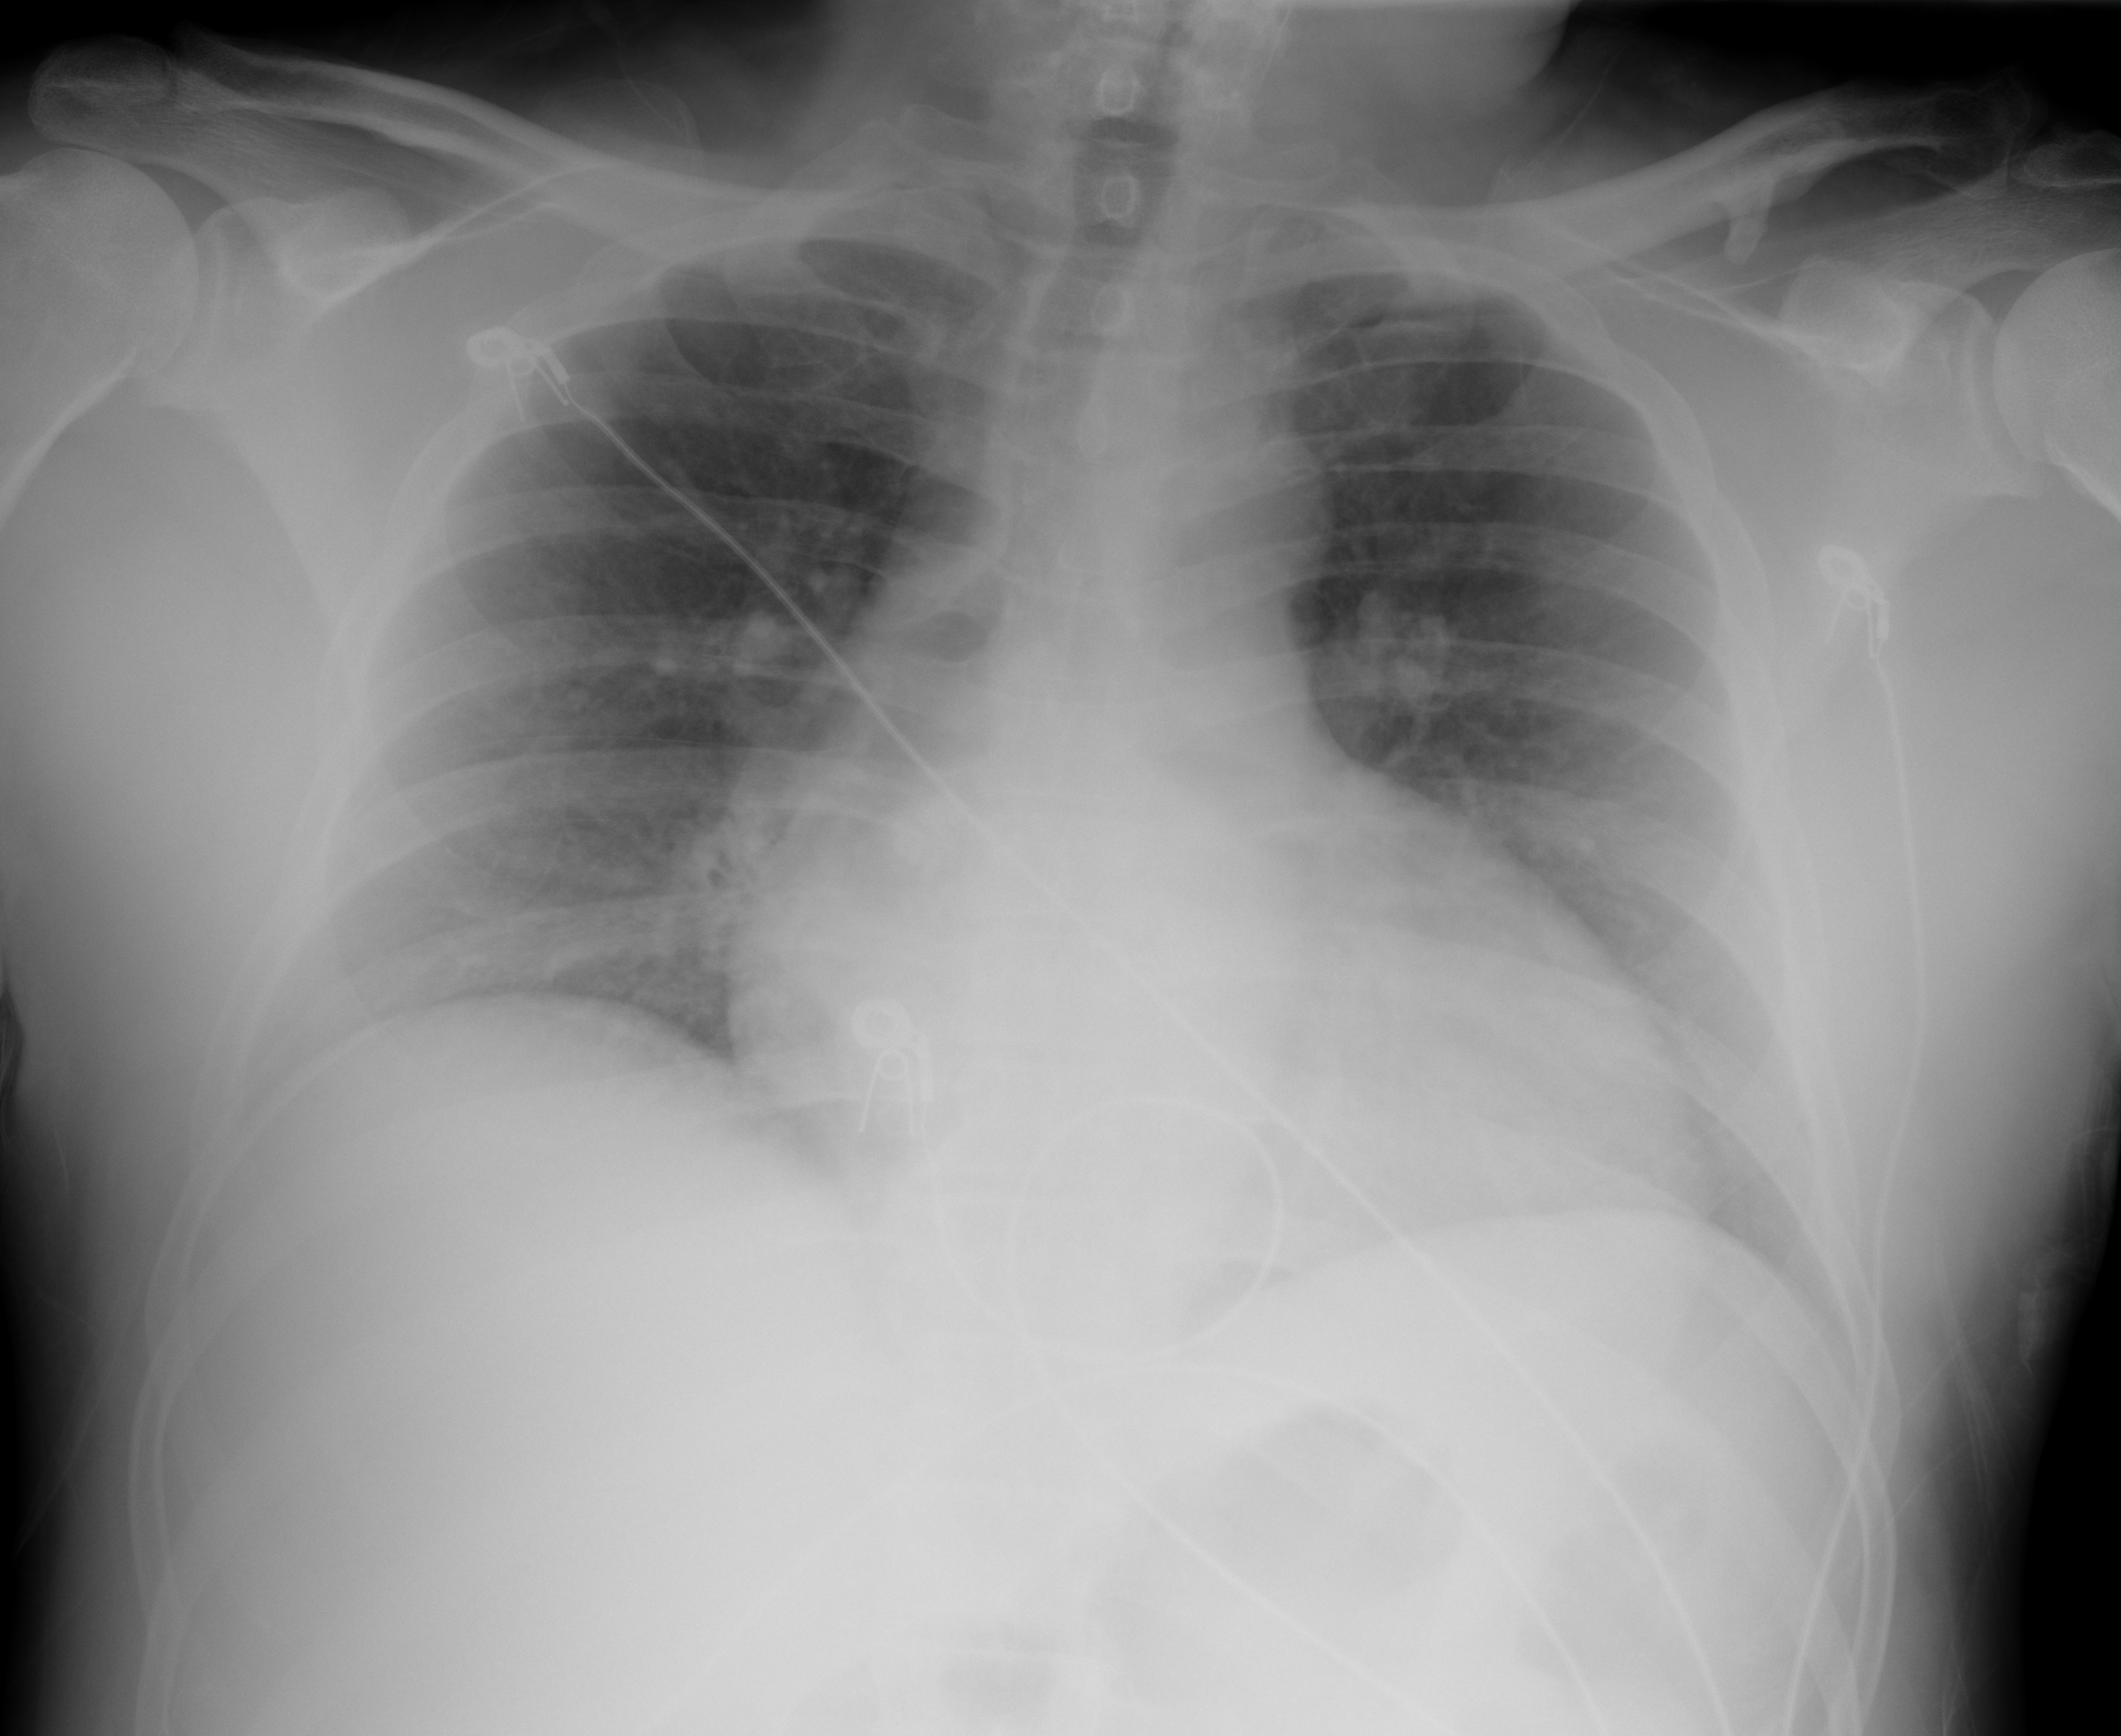
Chest X-ray (portable), AP projection. Male patient, age 49 years; COVID-19 (test-positive).
Radiologist key findings (as recorded): The lungs are free of air space disease.